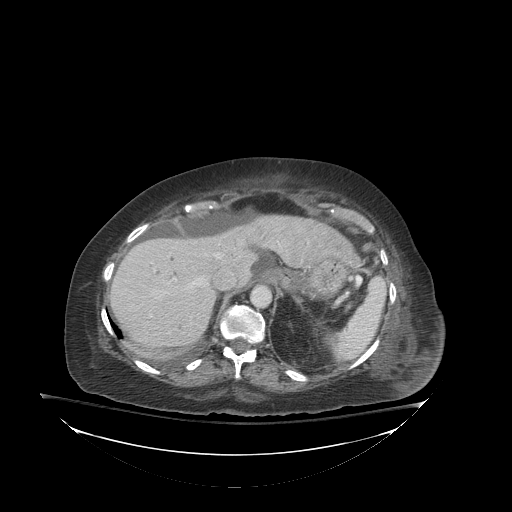
Contrast-enhanced abdominal CT (liver protocol), one axial slice. Slice 63 of 81 in the series (ordered by position). Reconstruction kernel STANDARD. 140 kVp. Soft-tissue window (W 400 / L 40 HU). 512 × 512 image matrix. From the clinical record (not read from this slice): diagnosis: hepatocellular carcinoma (patient treated with transarterial chemoembolisation; whether this scan precedes or follows treatment is not stated here); TNM stage (as recorded): Stage-I.
Structures marked on this image (semi-automatically segmented with operator editing):
- liver parenchyma outside the tumour (the mass and vessels are separate outlines, so this box may not span the whole liver): box from (x=110, y=216) to (x=322, y=350) px
- liver vessels: (x=192, y=254)–(x=218, y=285)